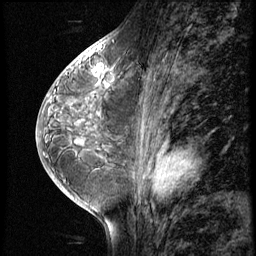
Breast MRI (dynamic contrast-enhanced), one sagittal slice. Position 30 of 56 along the scan axis. 3 images stored at this slice position (order not interpretable as contrast timing). 1.5 T. TE 4.2 ms, TR 8.9 ms. 2.5 mm slice thickness. 256 × 256 image matrix, field of view 200 × 200 mm. Female patient, age 38 years. Case-level facts recorded for this patient, not image findings: setting: breast cancer imaged before/during neoadjuvant chemotherapy; receptor status: triple-negative.
Annotated regions visible in this slice (semi-automatically segmented with operator editing):
- analysis volume of interest (the breast-tissue region the enhancement analysis was run in; not a lesion): bounding box <88,60,110,84> (left, top, right, bottom; pixels)
- tumour enhancement mask (voxels above the 140 % enhancement threshold inside the analysis volume of interest): <93,66,102,75>